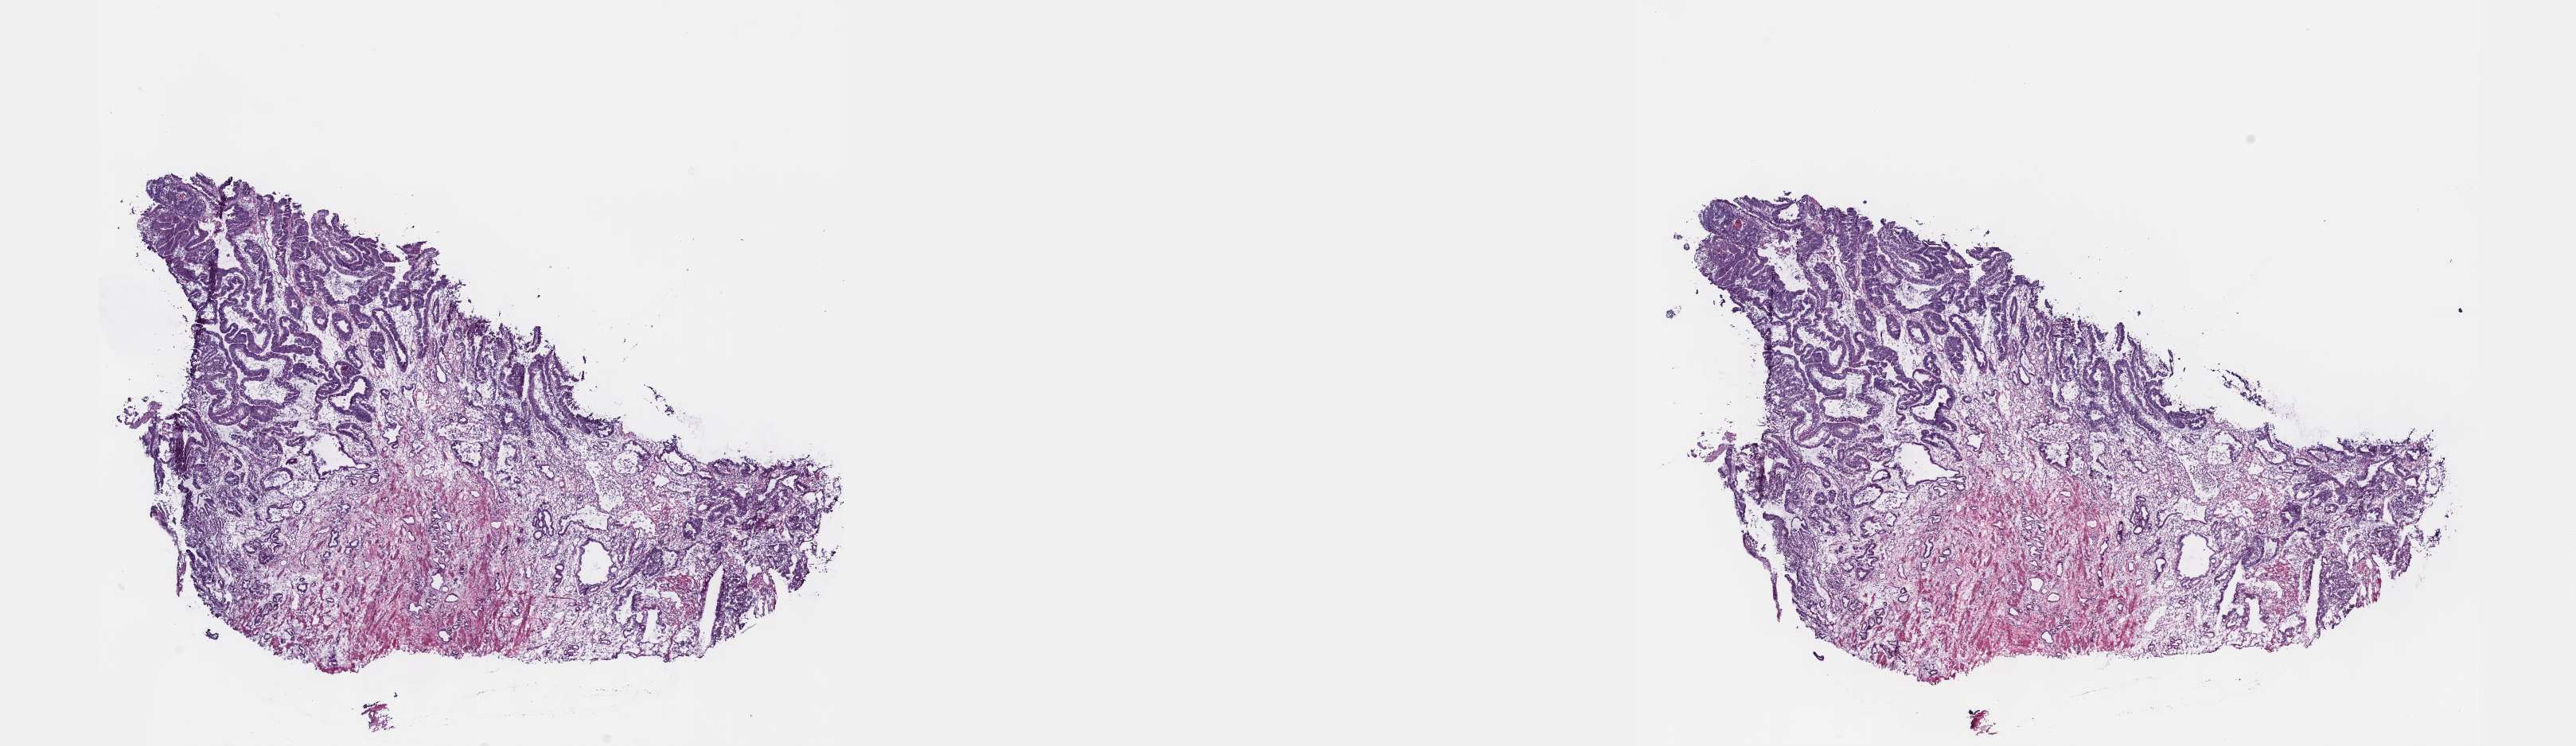
Digitized H&E-stained tissue section (whole slide), a low-resolution overview of the entire scanned area, about 26.2 x 7.6 mm (slide scanned at 40x); frozen section from the top of the tissue portion; sample: primary tumour, esophagus. Patient: male, age at initial diagnosis 57 years. Histologic grade: G2 (moderately differentiated). Pathologist review of this section (percent, as recorded): tumour cells 60%, tumour nuclei 60%, normal cells 0%, stromal cells 40%, necrosis 0%. Inflammatory infiltration, as recorded: lymphocyte infiltration 40%, monocyte infiltration 20%, neutrophil infiltration 20%.
AJCC pathologic stage: I (5th edition). Lymph nodes positive (case pathology): 0 of 19 examined. Diagnosis: Adenocarcinoma, NOS (lower third of esophagus).